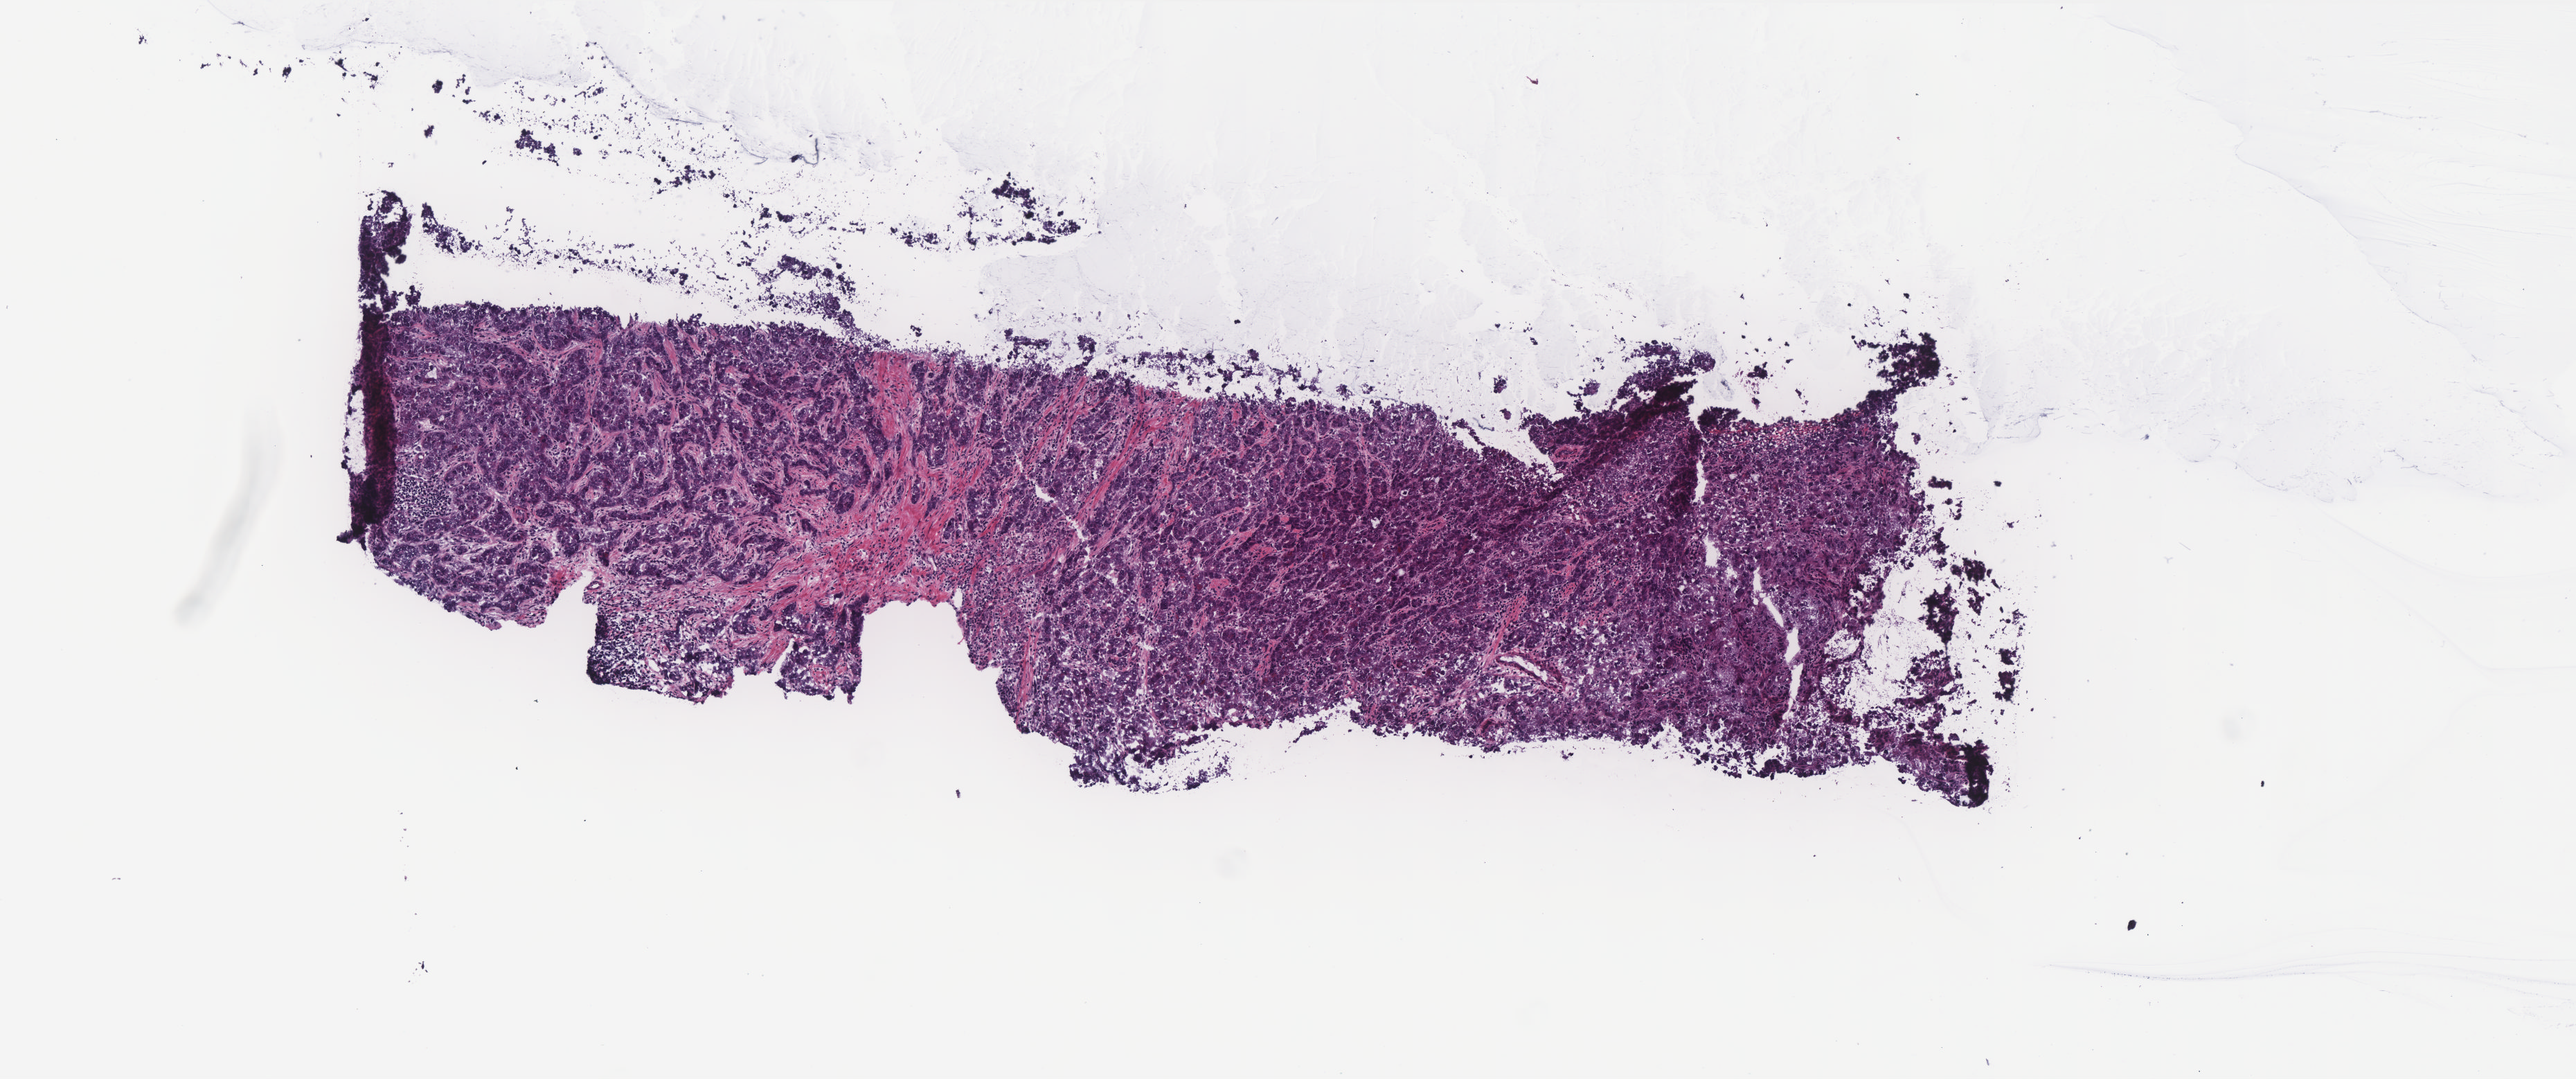
Whole-slide histology image, H&E, whole scanned area (about 7.5 x 3.1 mm, slide scanned at 40x) shown as a low-resolution overview. Frozen section from the top of the tissue portion. Liver, primary tumour sample. Patient: male, age at initial diagnosis 76 years. Histologic grade: G3 (poorly differentiated). Composition of this section per pathologist review: tumour cells 85%, tumour nuclei 85%, normal cells 0%, stromal cells 15%, necrosis 0%. Infiltration values recorded for this section: lymphocyte infiltration 5%, monocyte infiltration 0%, neutrophil infiltration 0%.
* AJCC pathologic stage: I (7th edition)
* histologic diagnosis: Hepatocellular carcinoma, NOS